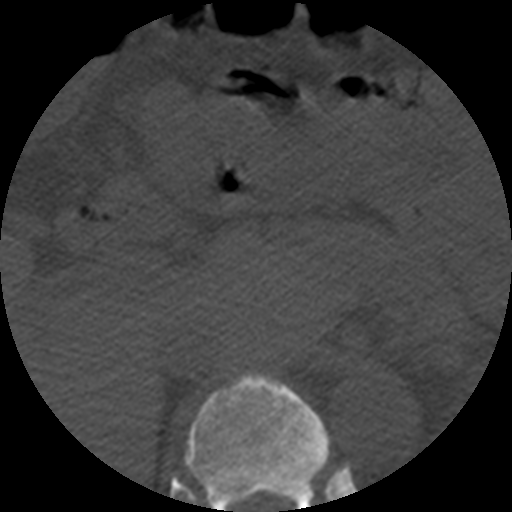
CT including the spine, one axial slice; slice 251 of 508 in the series (ordered by position); reconstruction kernel STANDARD; bone window (W 1800 / L 400 HU); 1.25 mm slice thickness; 512 × 512 image matrix, field of view 160 × 160 mm. Patient age 57 years. Case-level facts recorded for this patient, not image findings: primary cancer: prostate.
Structures marked on this image (semi-automatic segmentation, software-assisted and operator-edited):
- T11 vertebra: bounding box [x1, y1, x2, y2] px = [185, 372, 330, 512]